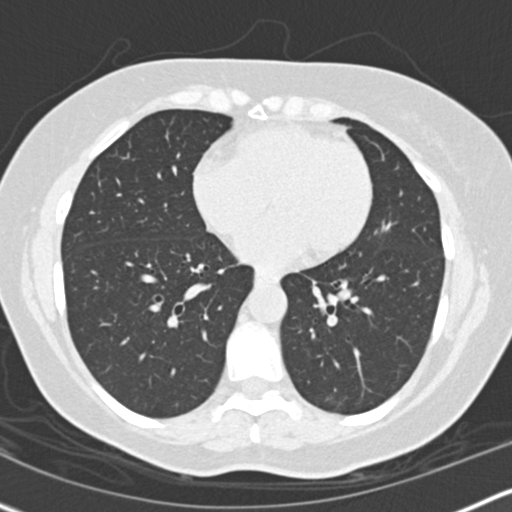
Low-dose screening chest CT, axial slice, second annual screen, lung window (W 1500 / L -600 HU), slice 90 of 158 in the series, 512 × 512 image matrix, field of view 310 × 310 mm. Female, age 56 years at enrolment. Former smoker at enrolment.
- Expert-annotated lung lesion, bounding box [x1, y1, x2, y2] px = [355, 202, 409, 256].
- Screening reader's record for this exam (one nodule recorded; not confirmed to be the boxed lesion): non-calcified nodule or mass ≥4 mm, lingula, 10 × 8 mm, smooth margins, soft tissue attenuation, pre-existing on the prior screen: yes; interval growth: yes.
- Participant outcome: lung cancer diagnosed 506 days after this screen (after the third annual screen) — adenocarcinoma, NOS, left upper lobe, poorly differentiated (G3), stage IIIA (AJCC 6th edition), 15 mm at pathology.